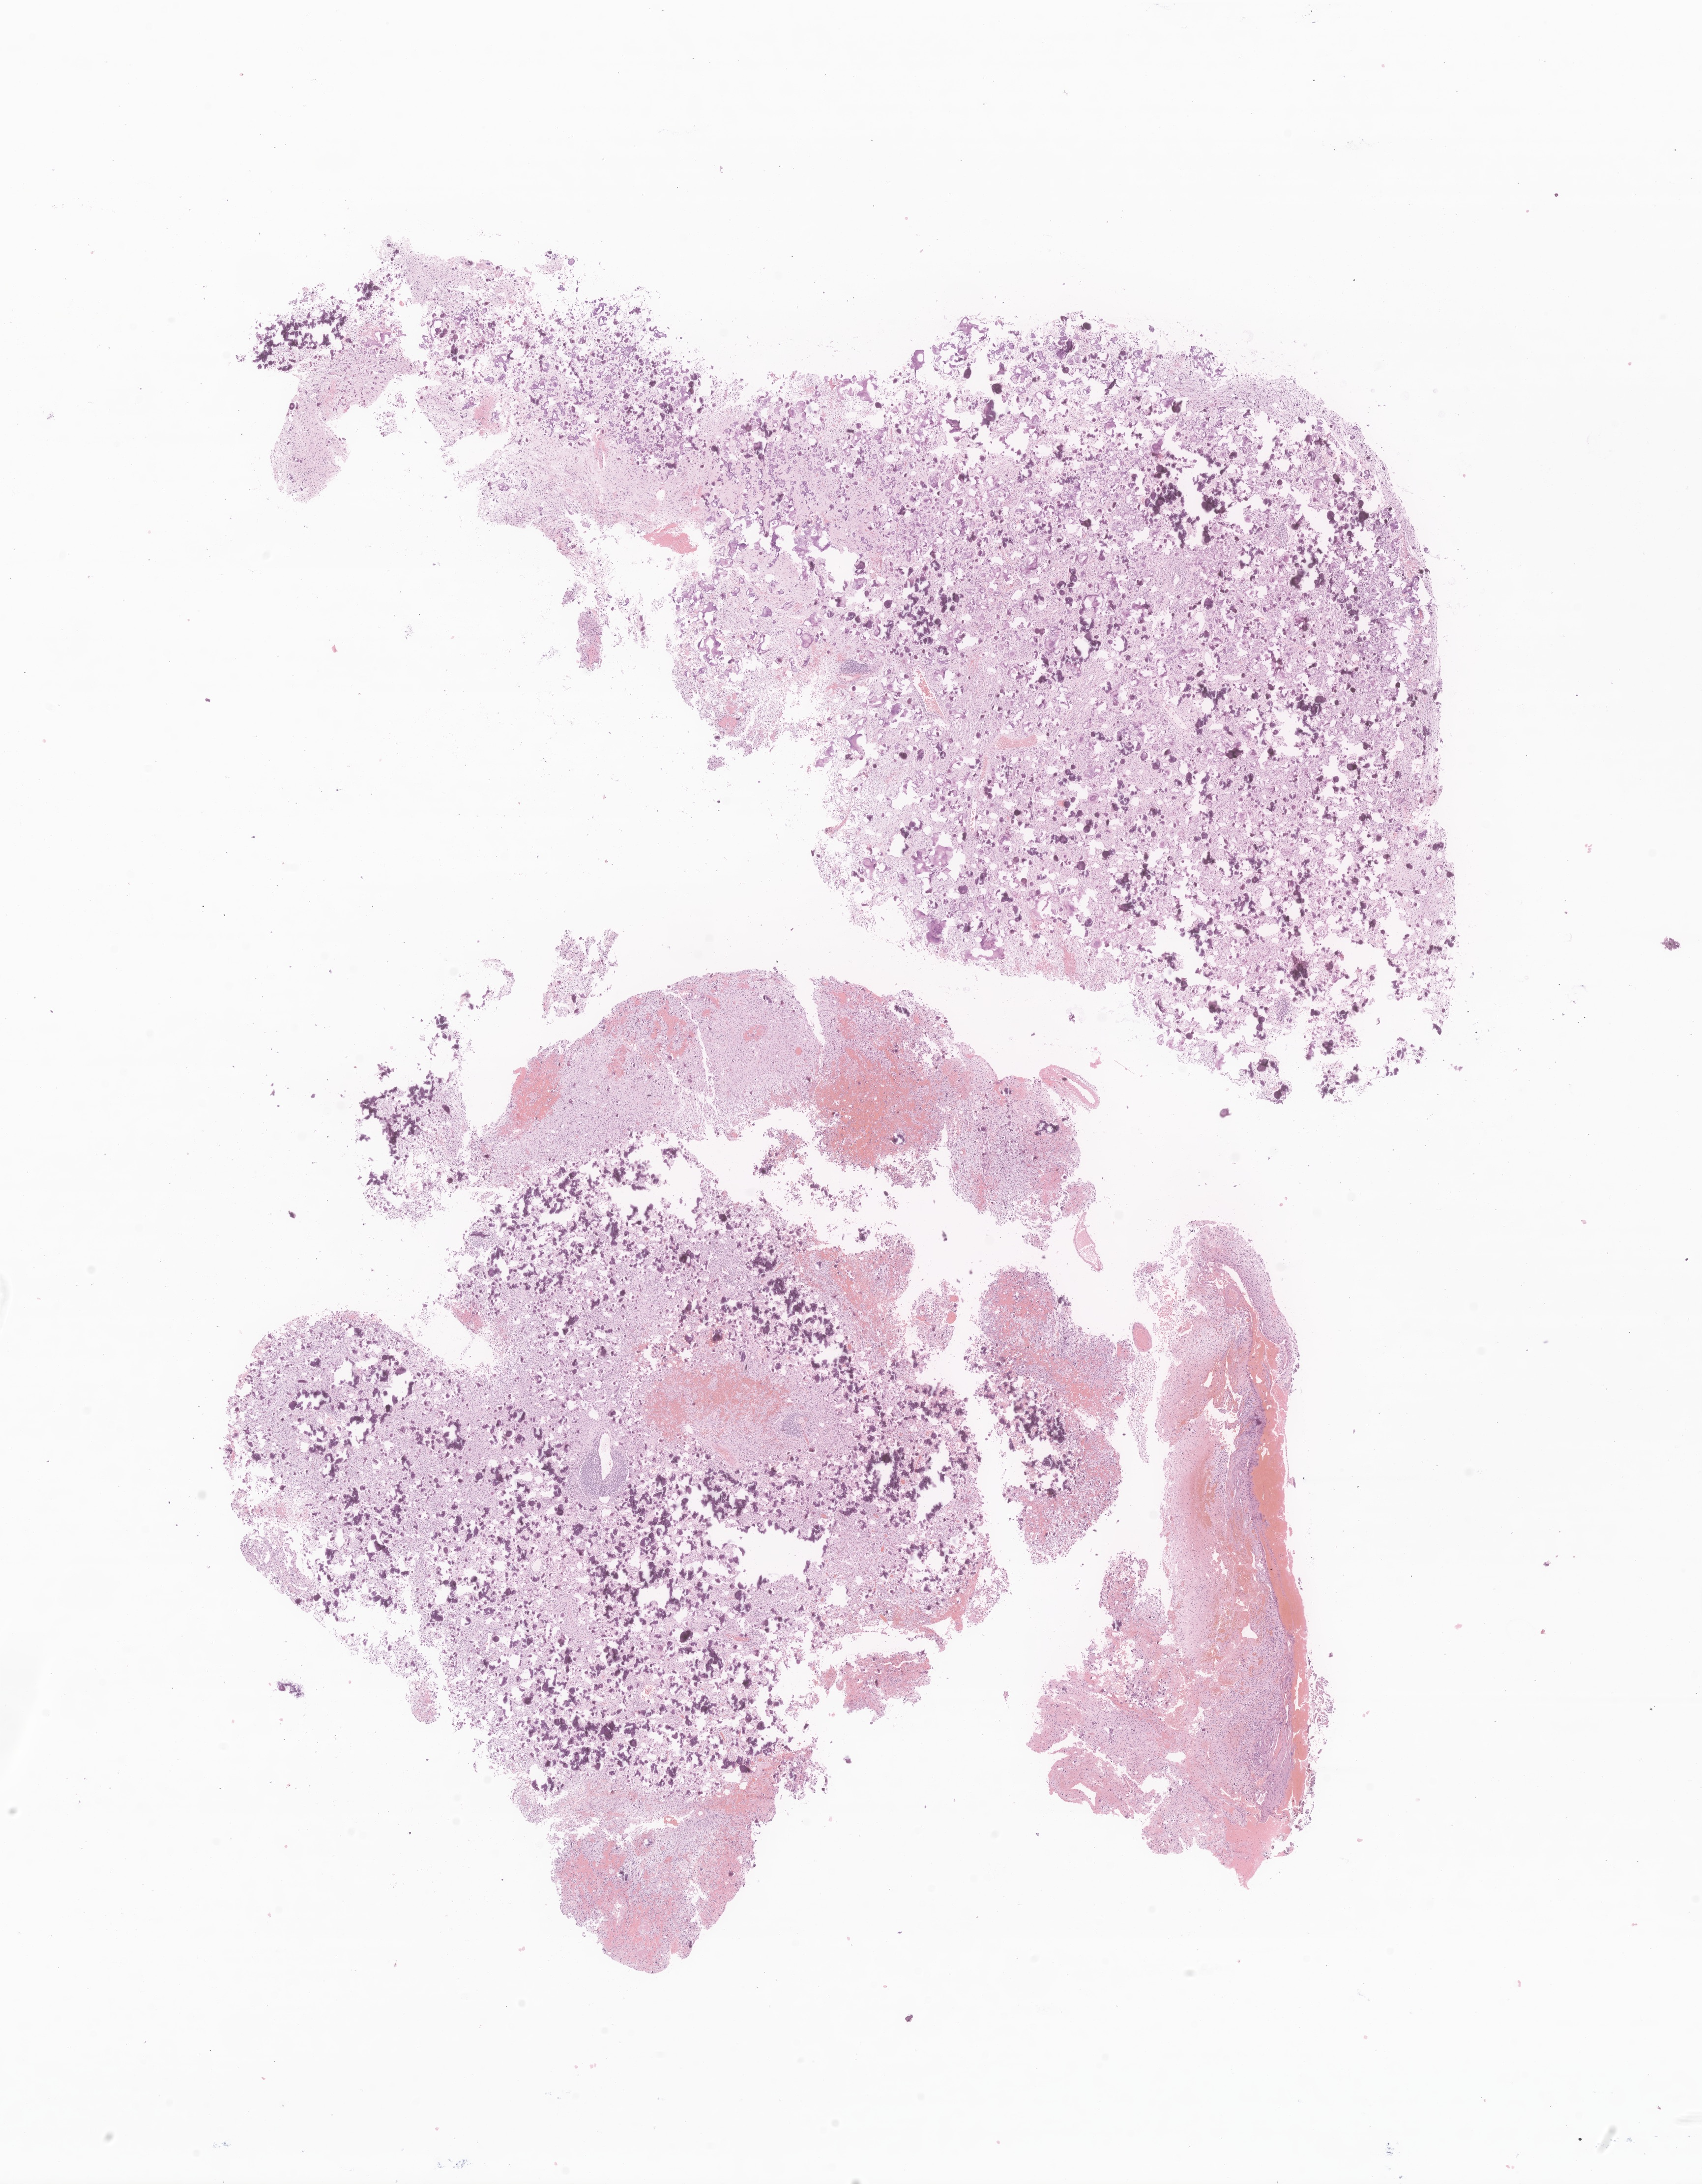
Whole-slide image, haematoxylin and eosin stain of tumor tissue from the brain, shown as a low-resolution overview of the whole scanned area (about 14.6 x 18.7 mm). Formalin-fixed, paraffin-embedded (FFPE) tissue. Patient: male, age 204 months (17 years).
- diagnosis: Glioma, malignant